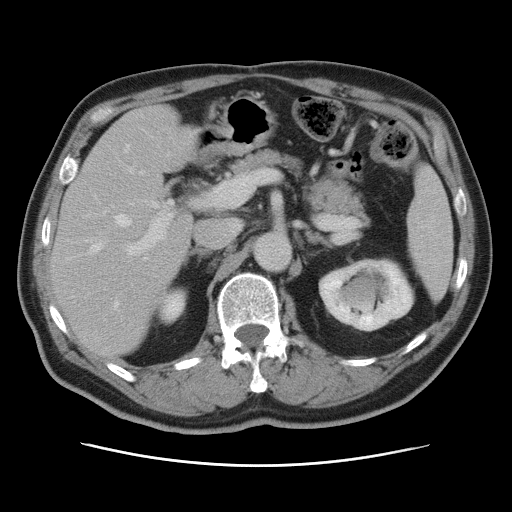
Contrast-enhanced abdominal CT, one axial slice. Slice 44 of 80 in the series (ordered by position). Intravenous contrast given. Soft-tissue window (W 400 / L 40 HU). 5 mm slice thickness. 512 × 512 image matrix, field of view 370 × 370 mm. Male patient, age 69 years. From the clinical record (not read from this slice): diagnosis: colorectal cancer liver metastases, imaged before liver resection; multiple liver metastases: no; largest metastasis: 5 cm; disease in both lobes: yes.
Annotated regions visible in this slice (outlined manually by an expert reader):
- hepatic veins: bounding box (x1, y1, x2, y2) in pixels: (87, 146, 146, 307)
- liver: (52, 107, 197, 356)
- planned liver remnant (the part of the liver to remain after resection): (52, 130, 198, 355)
- portal vein (with intrahepatic branches): (124, 167, 173, 257)